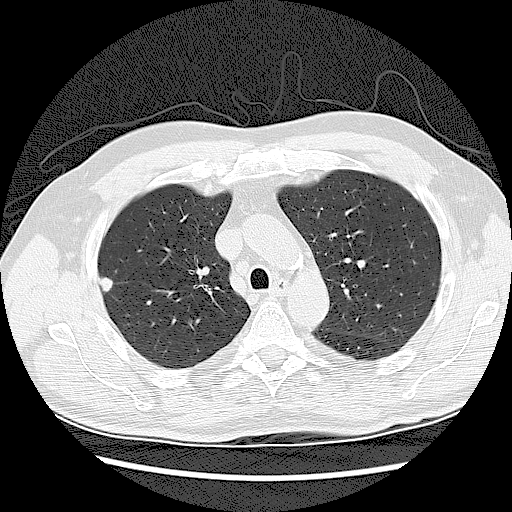
Low-dose screening chest CT, one axial slice; slice 85 of 120 in the series (ordered by position); reconstruction kernel LUNG; lung window (W 1500 / L -600 HU); 2.5 mm slice thickness; 512 × 512 image matrix.
Outlined on this slice (outlined manually by an expert reader):
- lesion 1 (tumor, upper lobe of right lung): bounding box (x1, y1, x2, y2) in pixels: (99, 277, 113, 294)